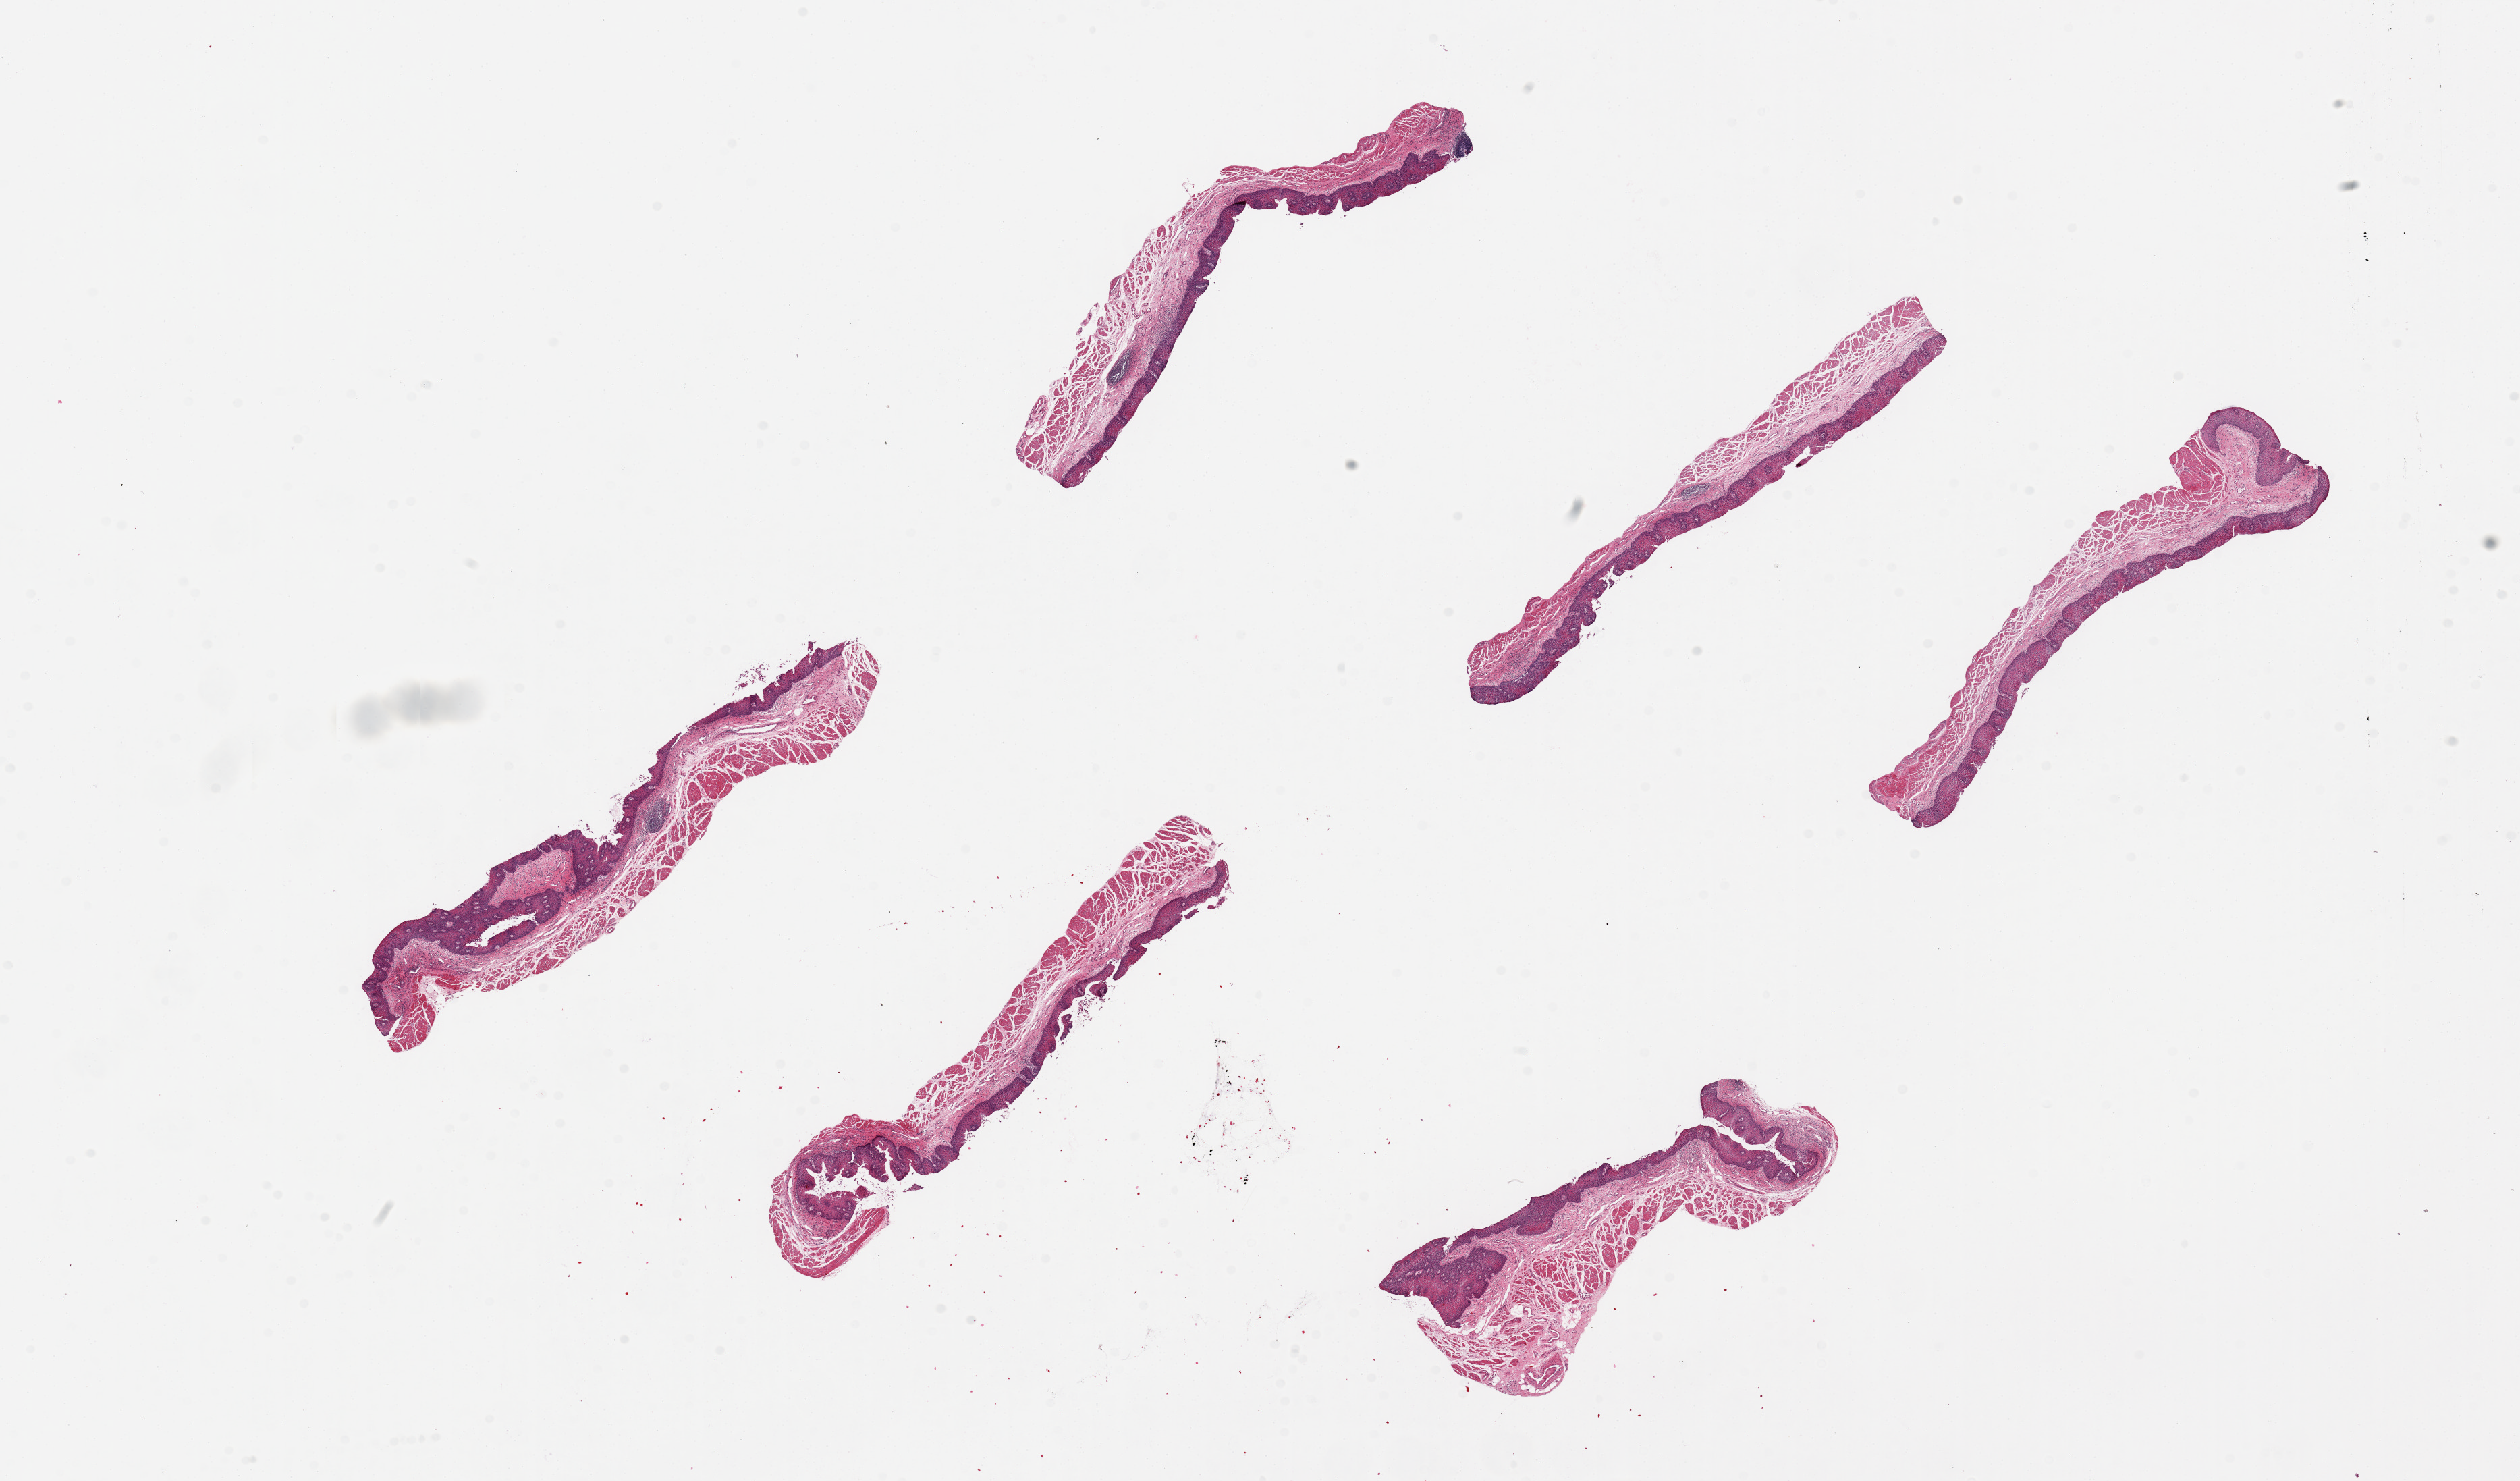
Whole-slide image, H&E stain — a low-resolution overview of the entire scanned area, about 29.5 x 17.4 mm; PAXgene-fixed, paraffin-embedded tissue; section of esophageal mucous membrane (target tissue); donor tissue sample. Donor sex: male.
* pathologist's review note for this sample: 6 pieces, up to 7x2mm; well dissected